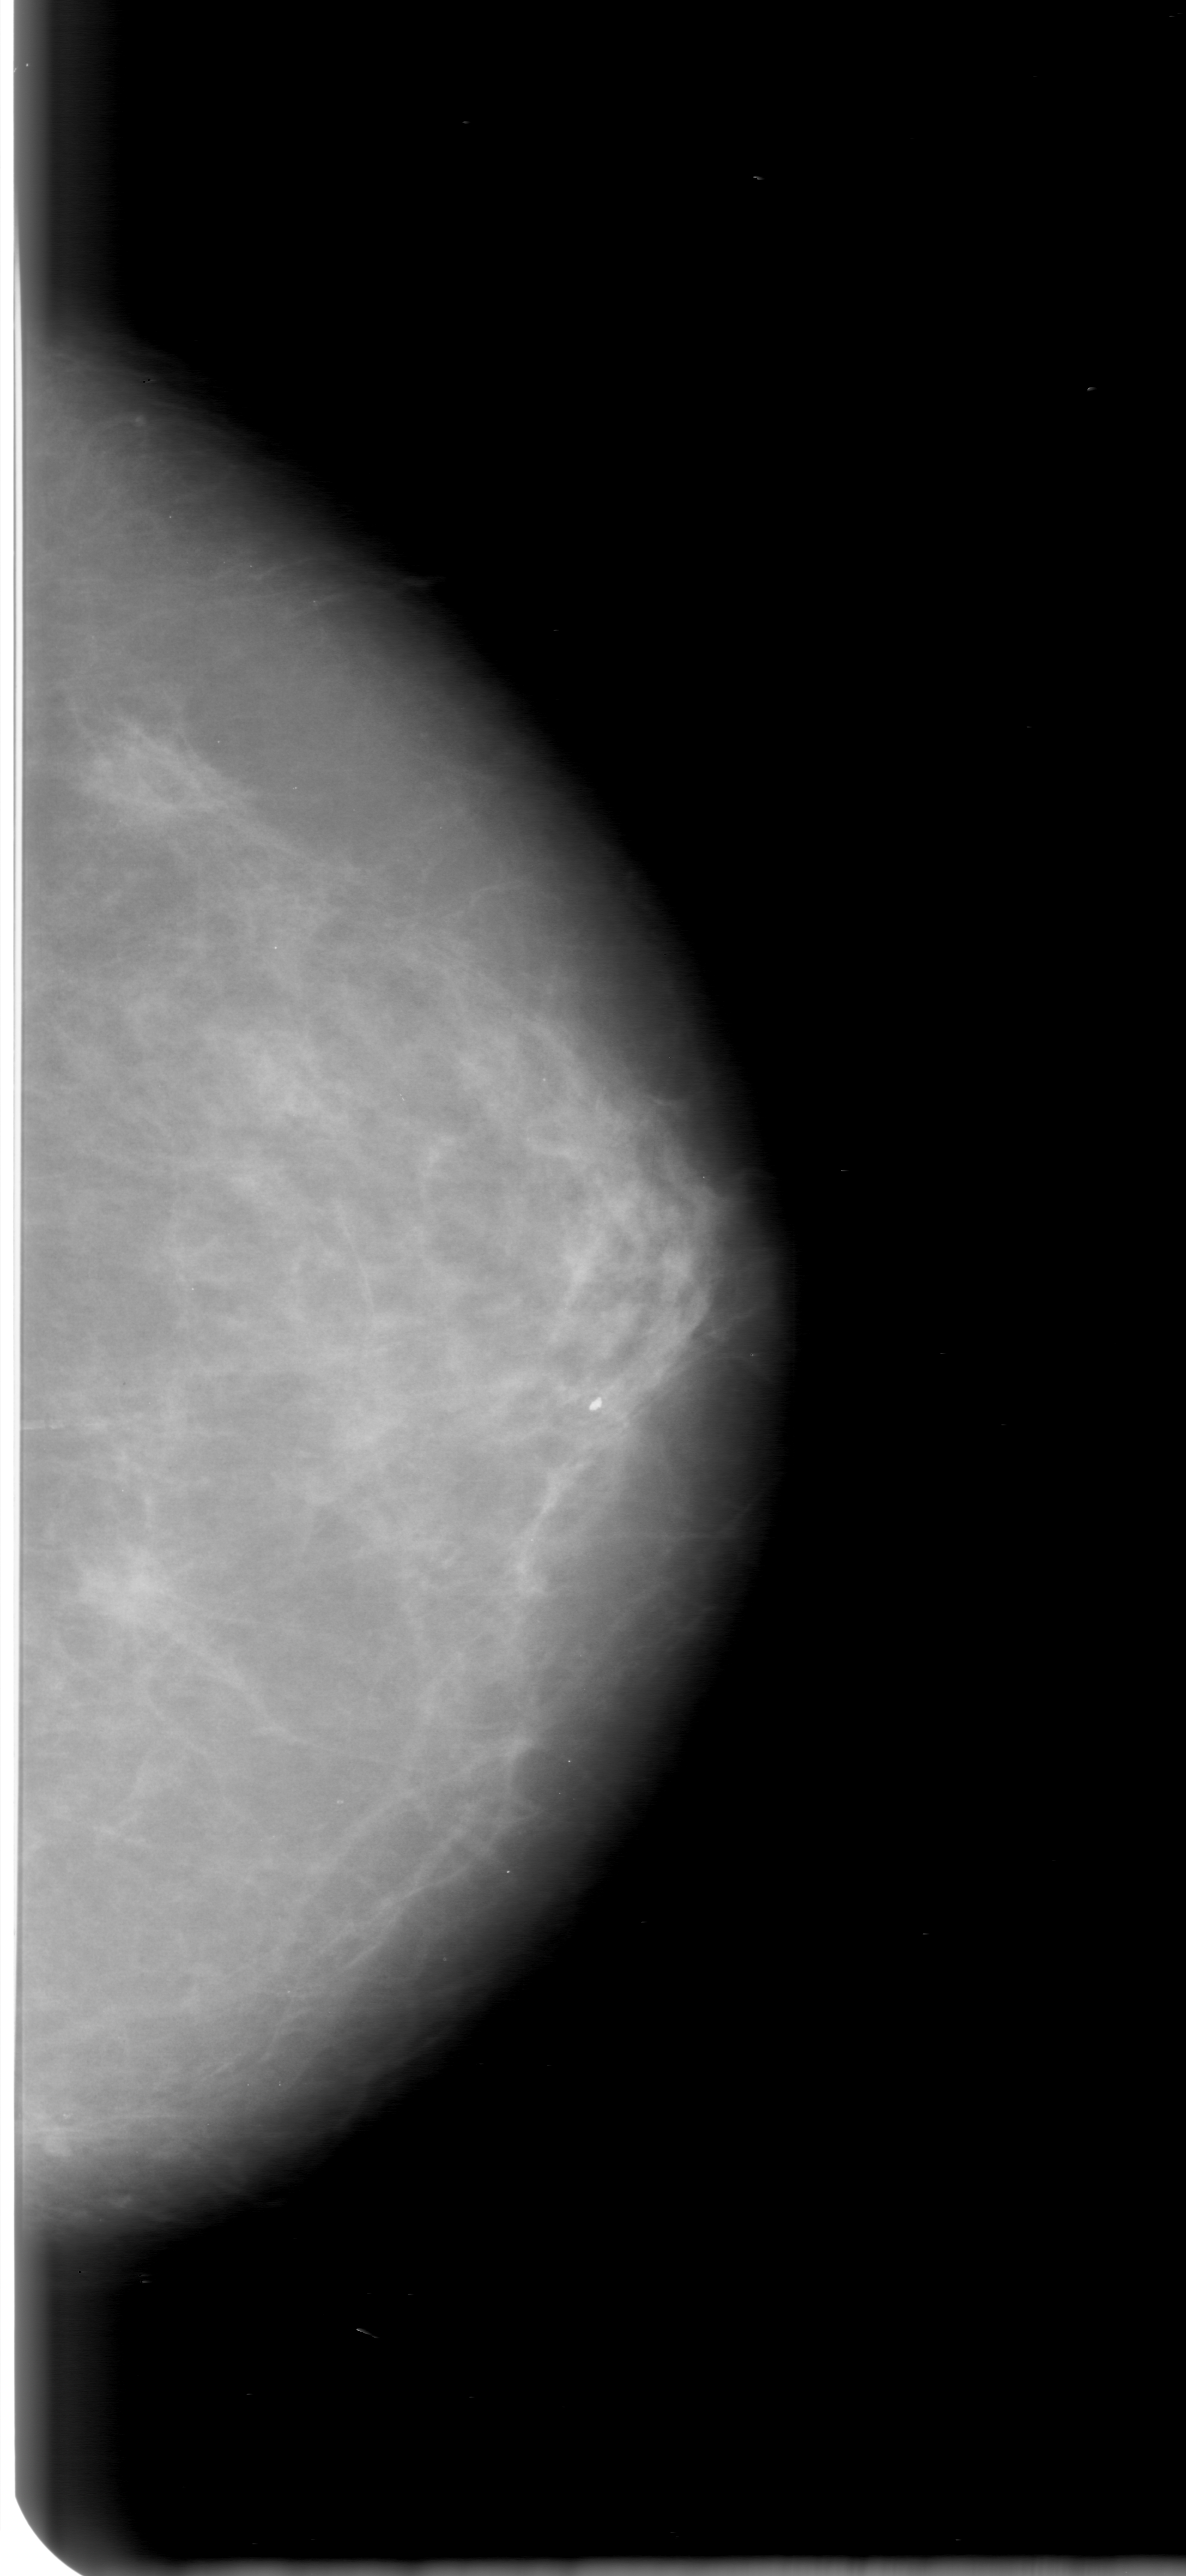
Scanned film-screen mammogram; left breast; craniocaudal (CC) view; 1186 × 2576 image matrix.
Marked abnormalities (boxes around the expert regions of interest):
- mass, shape irregular, margins ill defined; BI-RADS assessment category 2; subtlety rating 3 on a 1 (subtle) to 5 (obvious) scale; pathology result (as recorded, not read from the image): benign: bounding box <93,695,268,872> (left, top, right, bottom; pixels)